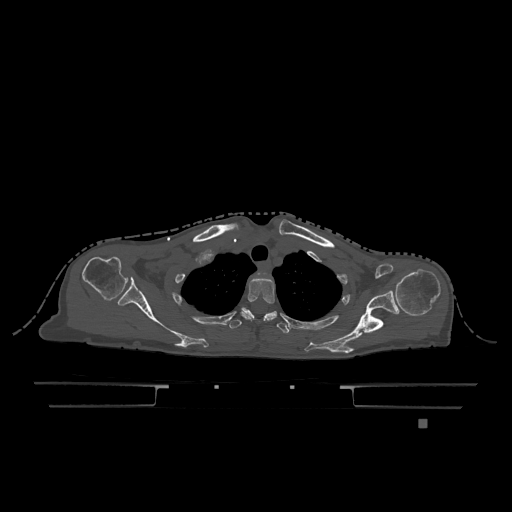
CT including the spine, one axial slice. Slice 951 of 1317 in the series (ordered by position). Bone window (W 1800 / L 400 HU). 0.5 mm slice thickness. 512 × 512 image matrix. Female patient, age 74 years. Case-level facts recorded for this patient, not image findings: primary cancer: lung; vertebrae with lytic lesions (as recorded): T1, T4, T5, T6, L4, L5.
Annotated regions visible in this slice (semi-automatic segmentation, software-assisted and operator-edited):
- T2 vertebra: bounding box [x1, y1, x2, y2] px = [240, 277, 277, 321]
- T3 vertebra: [229, 309, 289, 334]
- T6 vertebra: [242, 308, 277, 317]